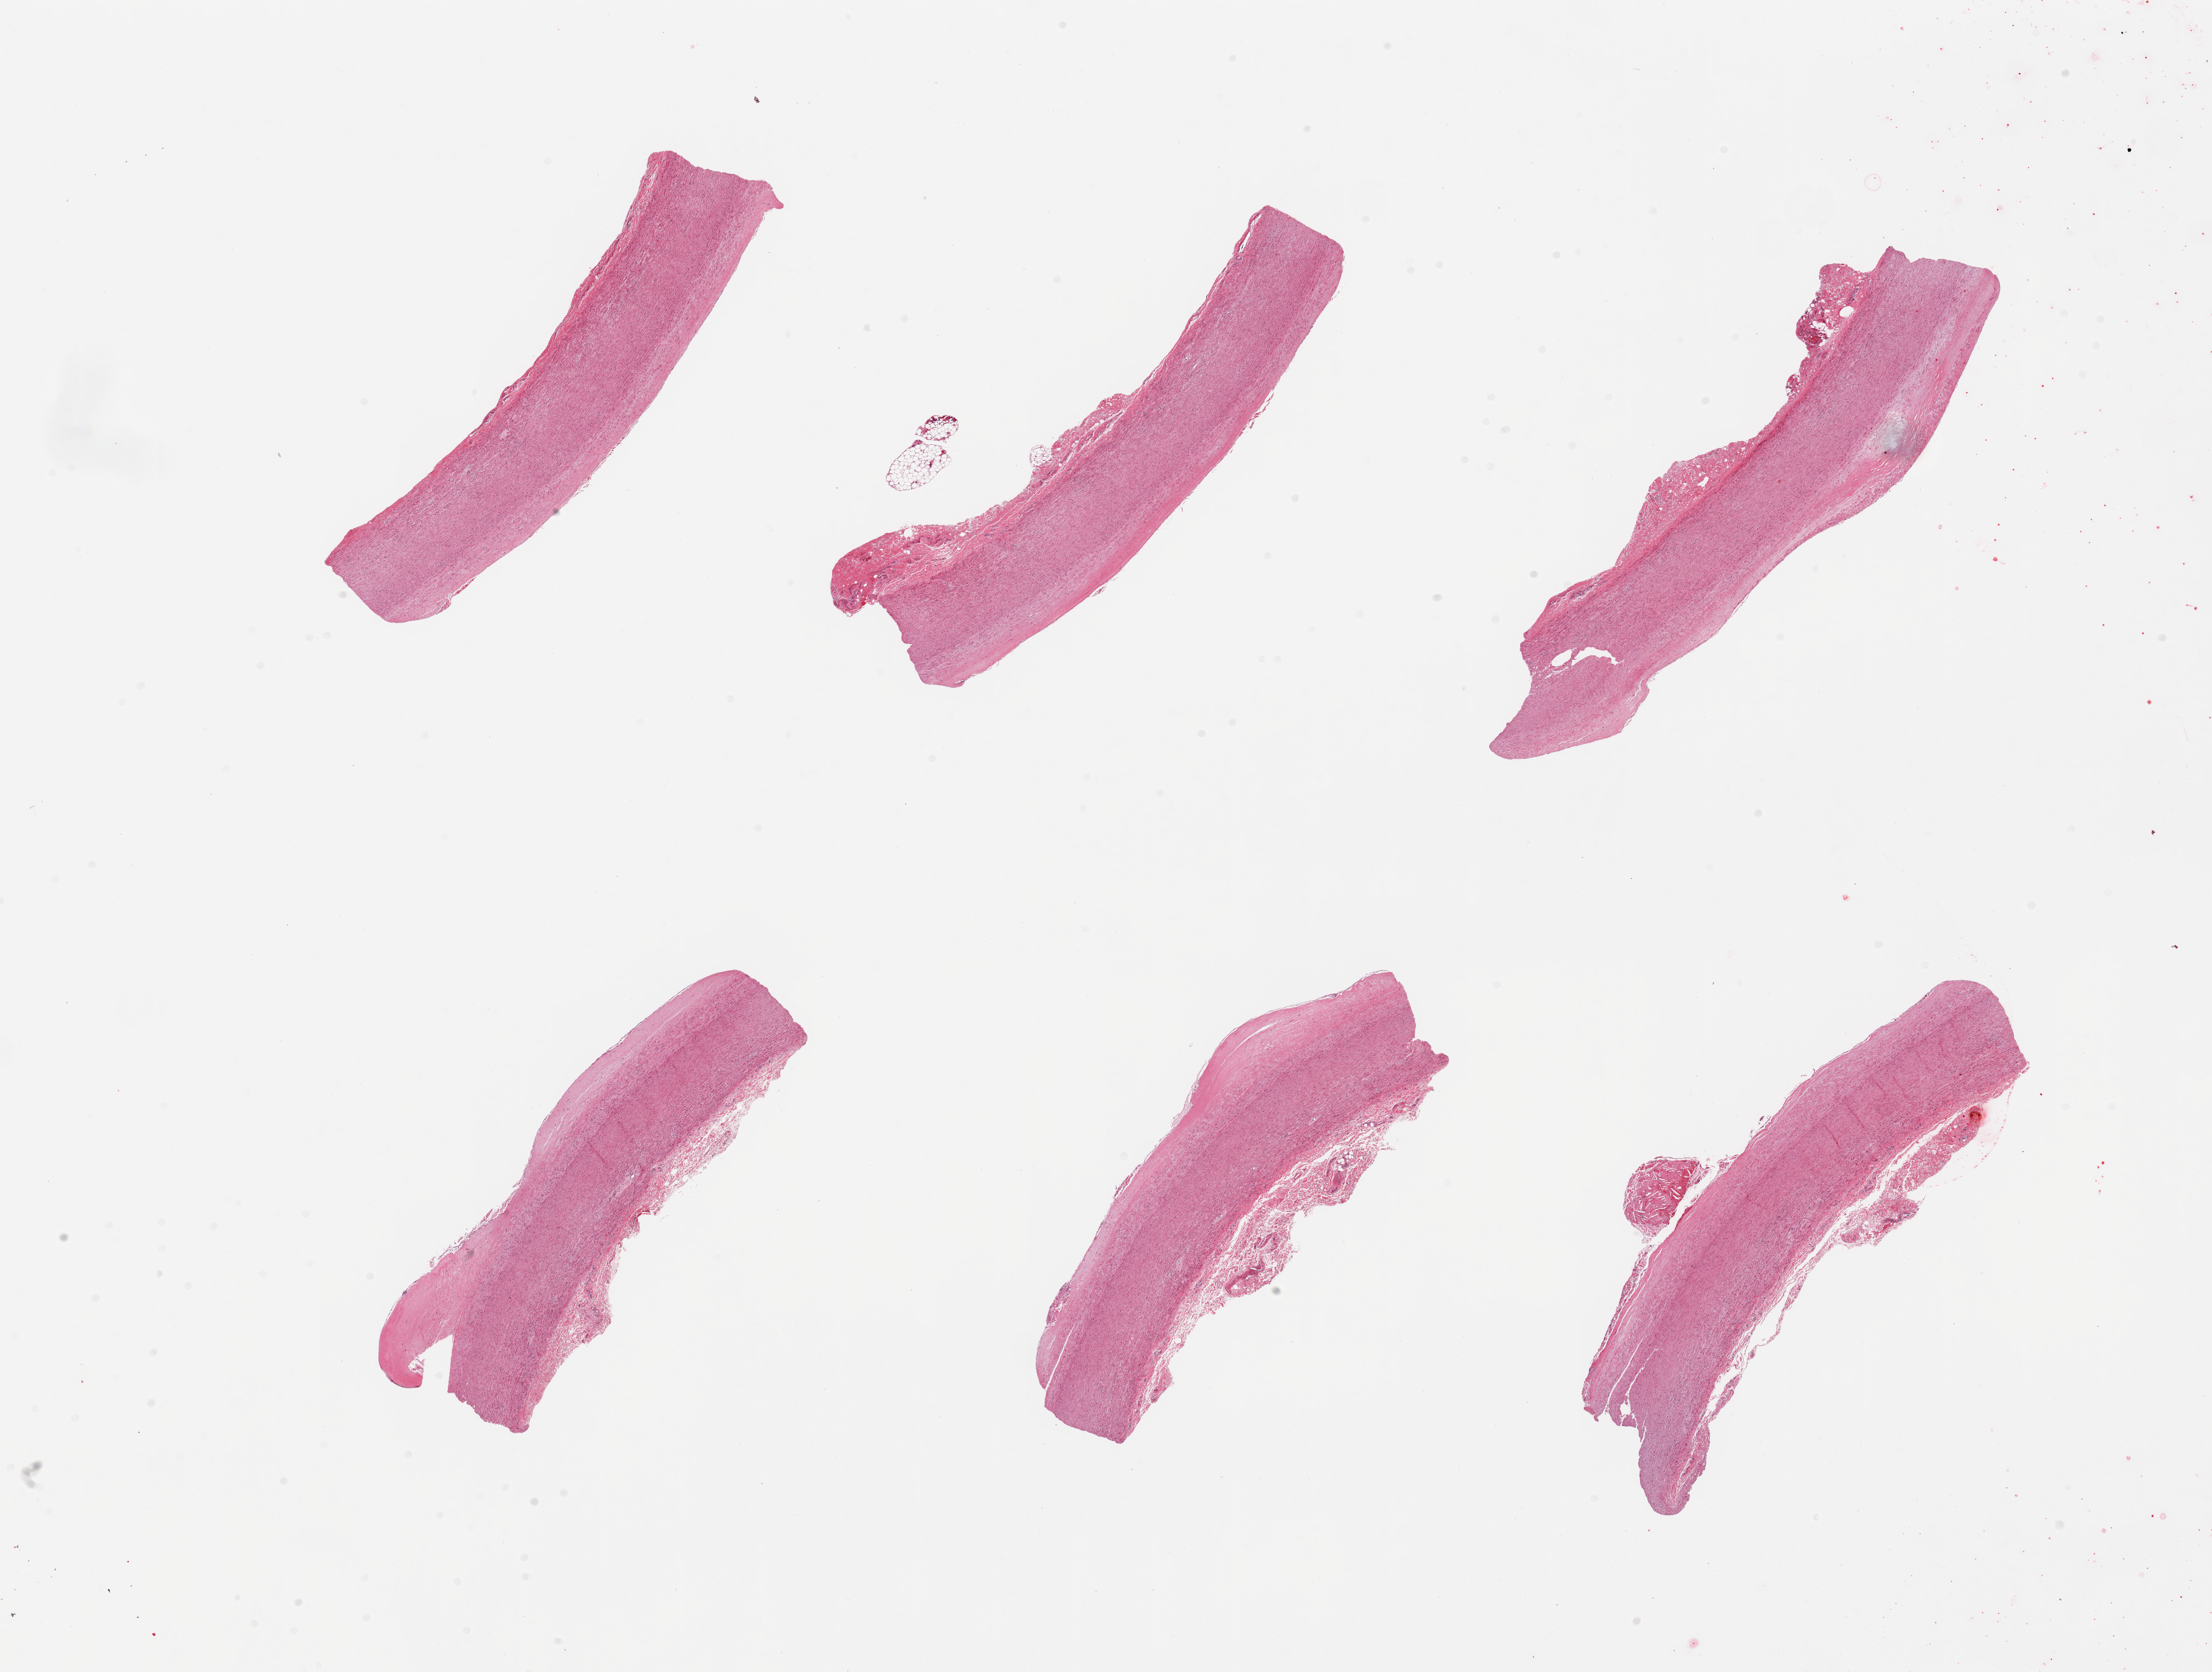
Digitized H&E-stained section — a low-resolution overview of the entire scanned area, about 27.6 x 20.8 mm; PAXgene-fixed paraffin-embedded (PFPE) section; sampled site (target tissue): aorta; tissue donor sample.
Review note (as recorded): 6 pieces; flat plaques; well trimmed.